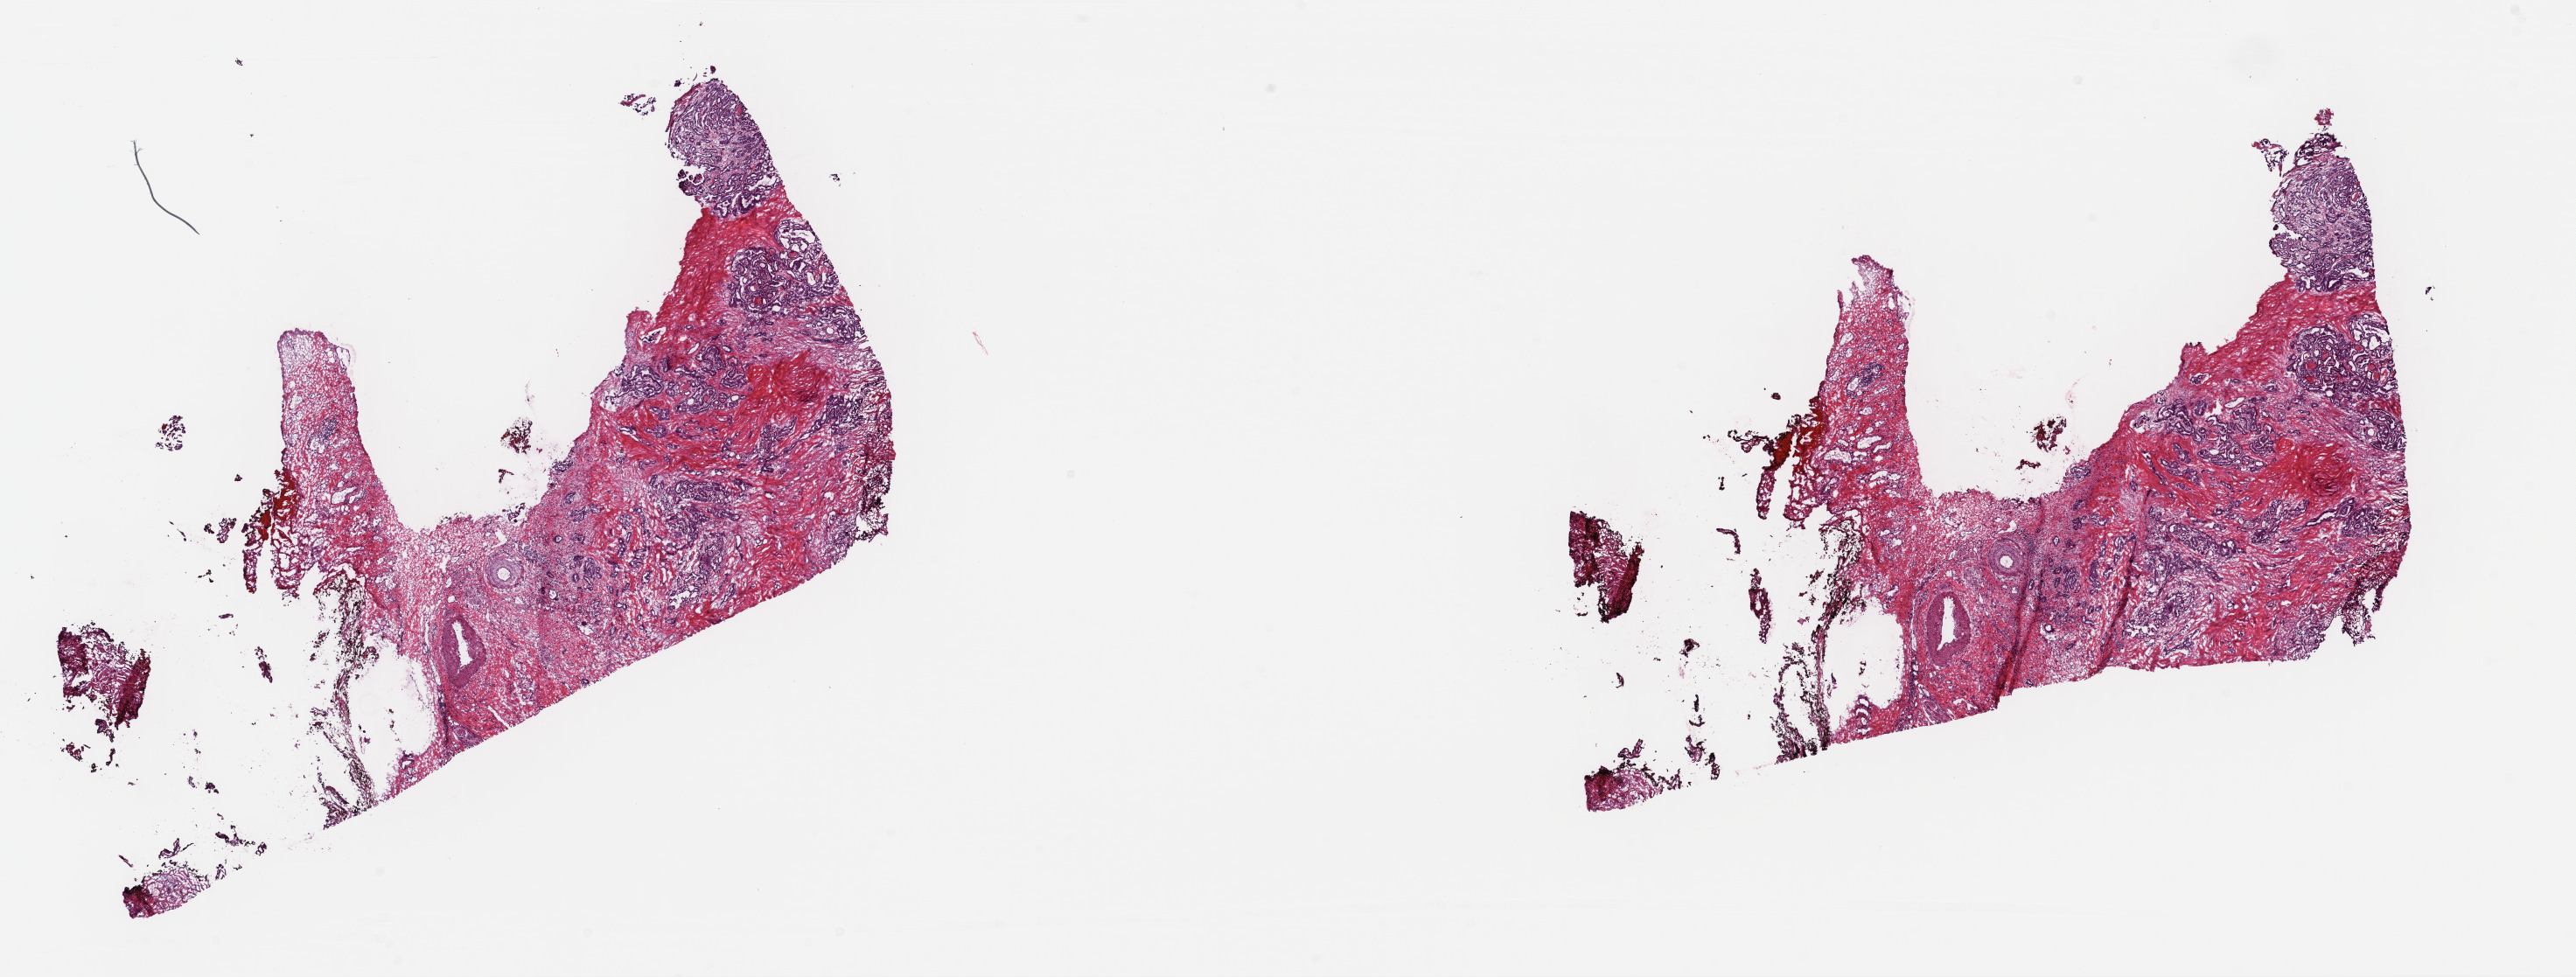
Whole-slide histology image, Hematoxylin and eosin (H&E) stained — low-resolution overview of the scanned area, about 23.3 x 8.8 mm (from a 40x scan). Frozen section. Sample: primary tumour, thyroid. Female, age 70 years at initial diagnosis. Pathologist review of this section (percent, as recorded): tumour cells 30%, tumour nuclei 100%, normal cells 0%, stromal cells 70%, necrosis 0%. Inflammatory infiltration, as recorded: lymphocyte infiltration 0%, monocyte infiltration 1%, neutrophil infiltration 0%.
* AJCC pathologic stage: III (7th edition)
* diagnosis: Papillary adenocarcinoma, NOS (thyroid gland)